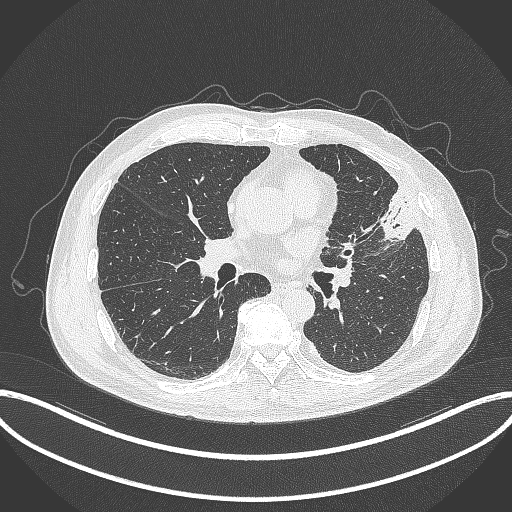
Chest CT, one axial slice; slice 169 of 382 in the series (ordered by position); reconstruction kernel B70f; lung window (W 1500 / L -600 HU); 512 × 512 image matrix, field of view 415 × 415 mm. Male patient, age 64 years. From the clinical record (not read from this slice): clinical TNM (as recorded): T4 N1 M0; histopathological grade: G3.
Annotated regions visible in this slice (bounding box drawn by a radiologist):
- lung tumour (recorded histology: adenocarcinoma): bounding box (x1, y1, x2, y2) in pixels: (376, 187, 417, 246)